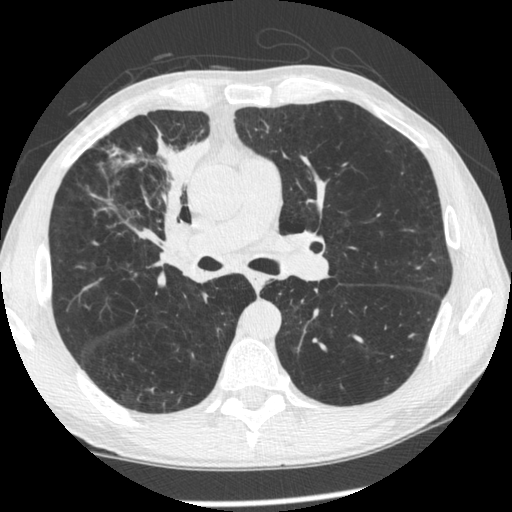
Low-dose screening chest CT, one axial slice; position 137 of 261 along the scan axis; 120 kVp; lung window (W 1500 / L -600 HU); 1.25 mm slice thickness; 512 × 512 image matrix, field of view 340 × 340 mm.
Outlined on this slice (outlined manually by an expert reader):
- lesion 1 (tumor, upper lobe of right lung): bounding box <157,135,210,236> (left, top, right, bottom; pixels)